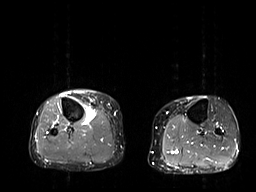
MRI of an extremity soft-tissue mass, one axial slice; position 18 of 32 along the scan axis; STIR; 6 mm slice thickness; 256 × 192 image matrix, field of view 375 × 281 mm. Female patient. Case-level facts recorded for this patient, not image findings: histological type: undifferentiated – high grade; grade: high; site of the primary tumour: right thigh.
Annotated regions visible in this slice (manually delineated by an expert):
- gross tumour volume (mass): bounding box <83,106,96,124> (left, top, right, bottom; pixels)